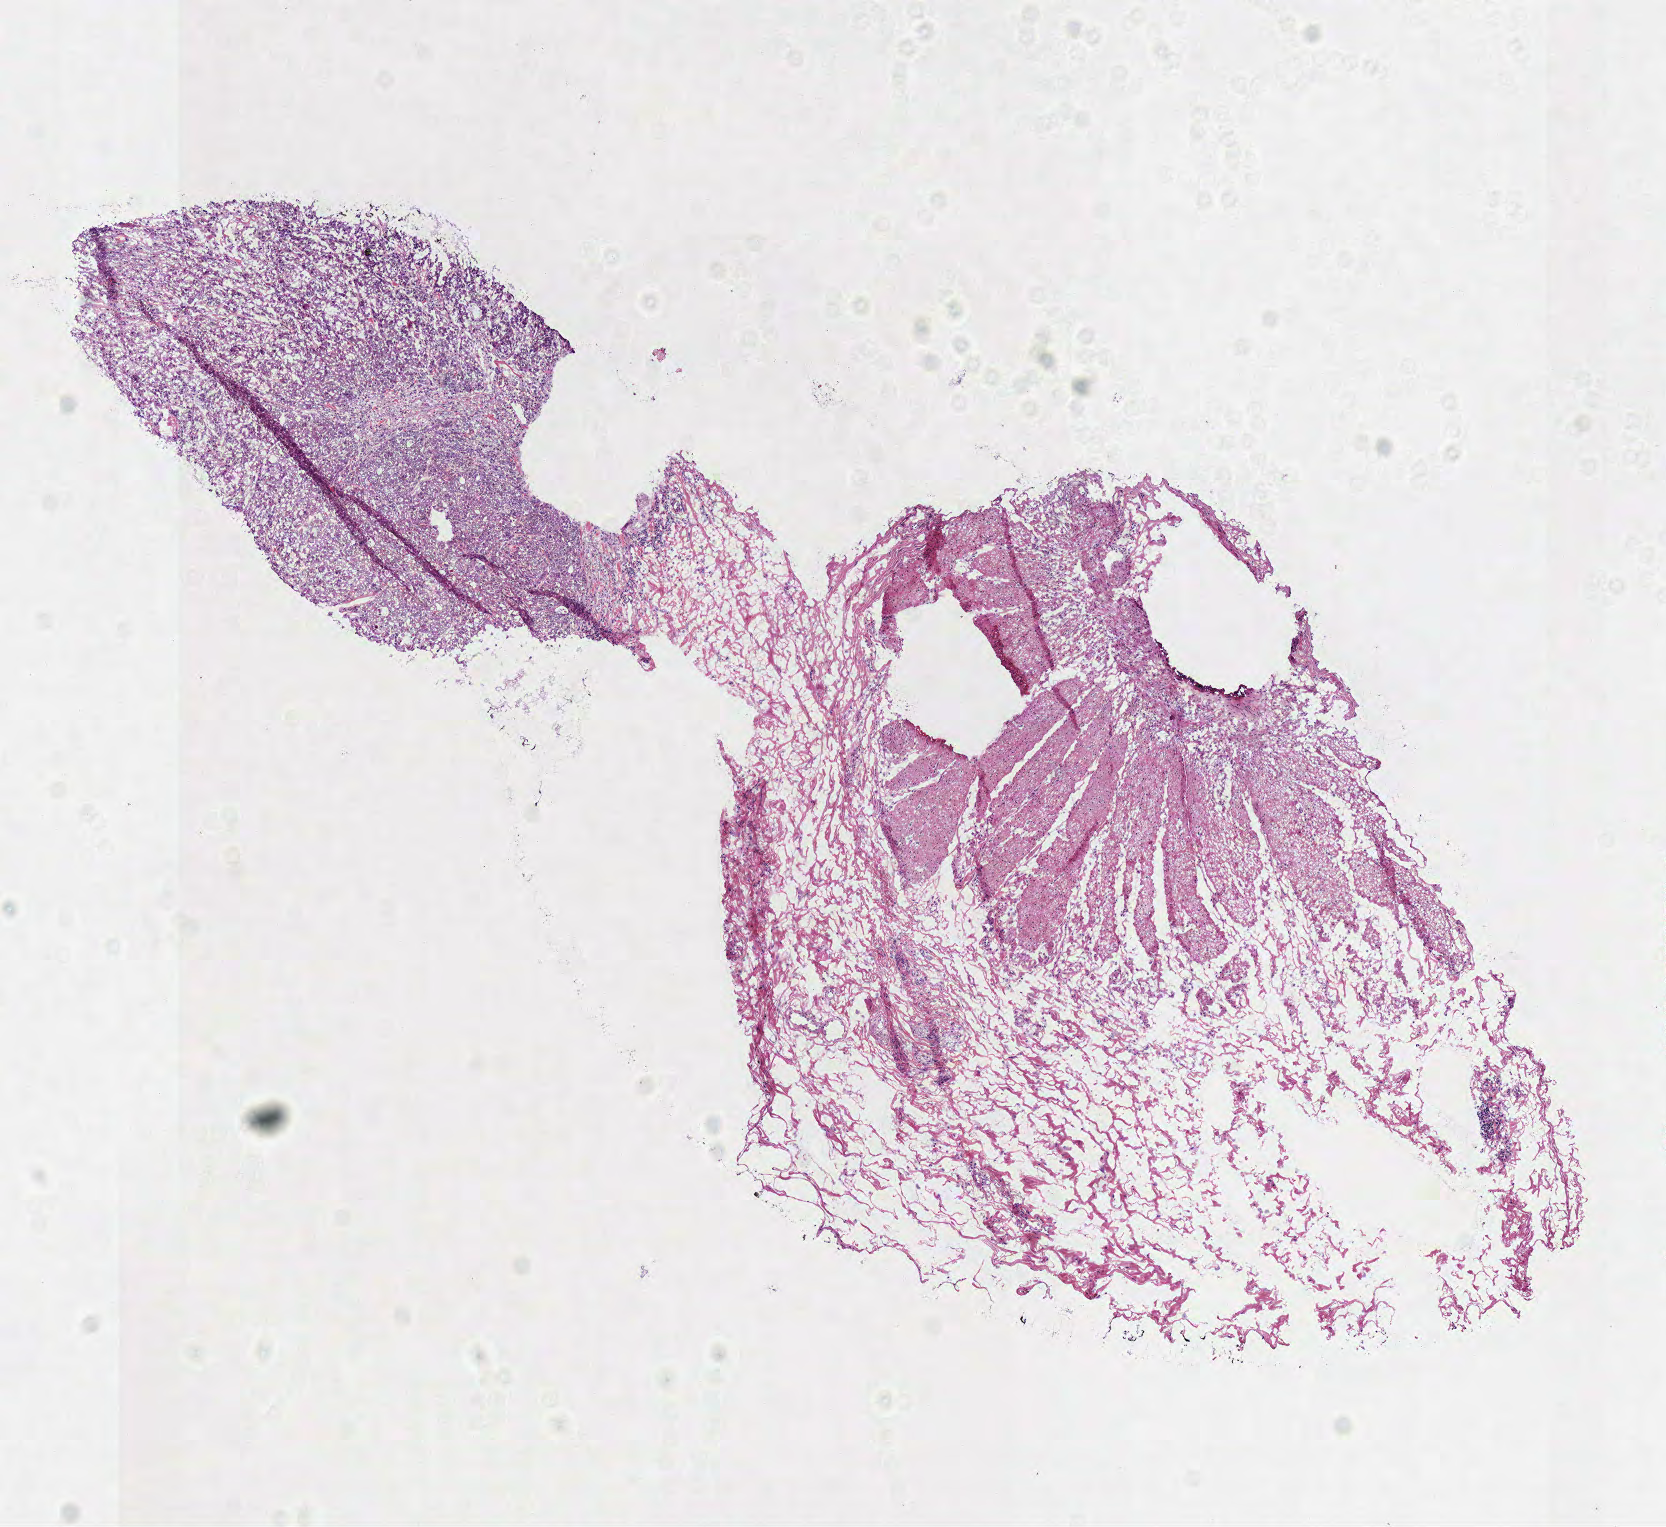
H&E whole-slide image, a low-resolution overview of the entire scanned area, about 6.6 x 6.0 mm (from a 40x scan); frozen section; primary tumour sample from the colon. Male, age 84 years at initial diagnosis. Composition of this section per pathologist review: tumour cells 85%, tumour nuclei 80%.
Histologic diagnosis: Adenocarcinoma, NOS.